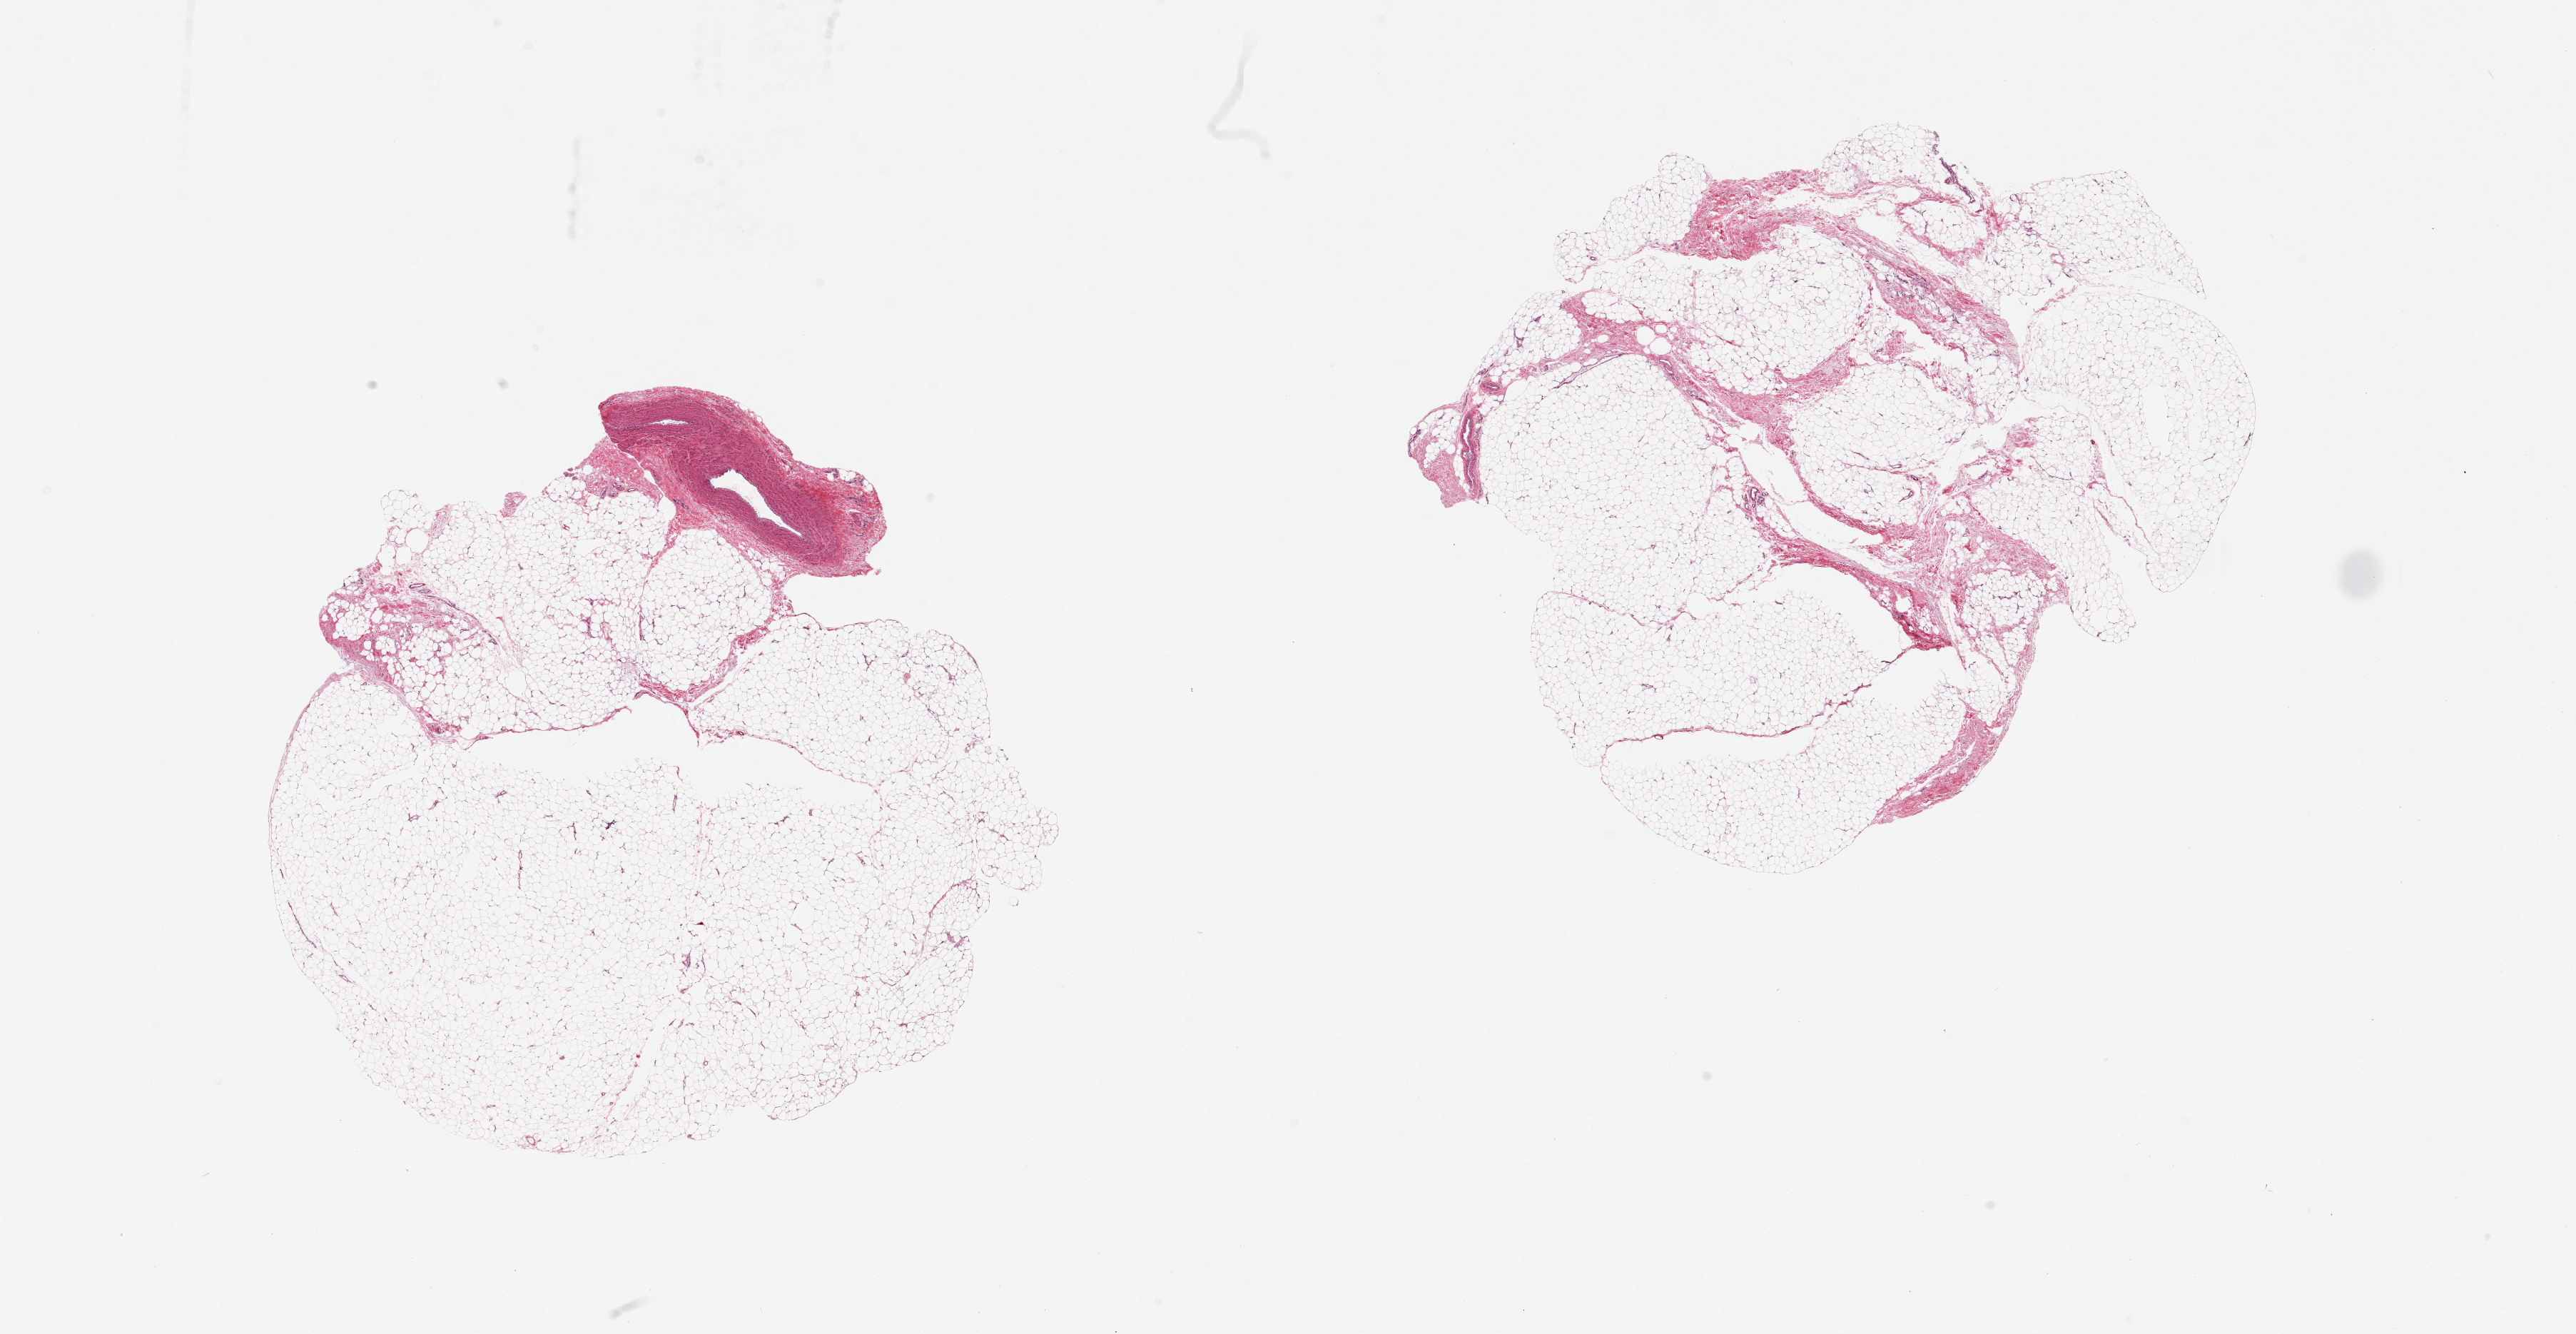
Hematoxylin and eosin (H&E) whole-slide image, brightfield — shown as a low-resolution overview of the whole scanned area (about 28.5 x 14.8 mm, acquisition: 20x scan); PAXgene-fixed, paraffin-embedded tissue; target tissue: adipose tissue; tissue donor sample. Donor sex: female.
* review note (as recorded): 2 pieces, one is fat with attached larger vessel, second has ~15% fibrovascular tissue